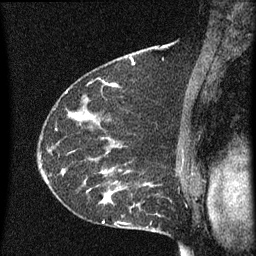
Breast MRI (dynamic contrast-enhanced), one sagittal slice; slice 41 of 60 in the series (ordered by position); dynamic contrast-enhanced series, image 2 of 3 at this slice position (ordered by acquisition); 1.5 T; TE 4.2 ms, TR 8 ms; 2 mm slice thickness; 256 × 256 image matrix. Female patient, age 55 years.
Outlined on this slice (semi-automatic segmentation, software-assisted and operator-edited):
- analysis volume of interest (the breast-tissue region the enhancement analysis was run in; not a lesion): bounding box <51,156,145,217> (left, top, right, bottom; pixels)
- tumour enhancement mask (voxels above the 70 % enhancement threshold inside the analysis volume of interest): <87,170,145,209>